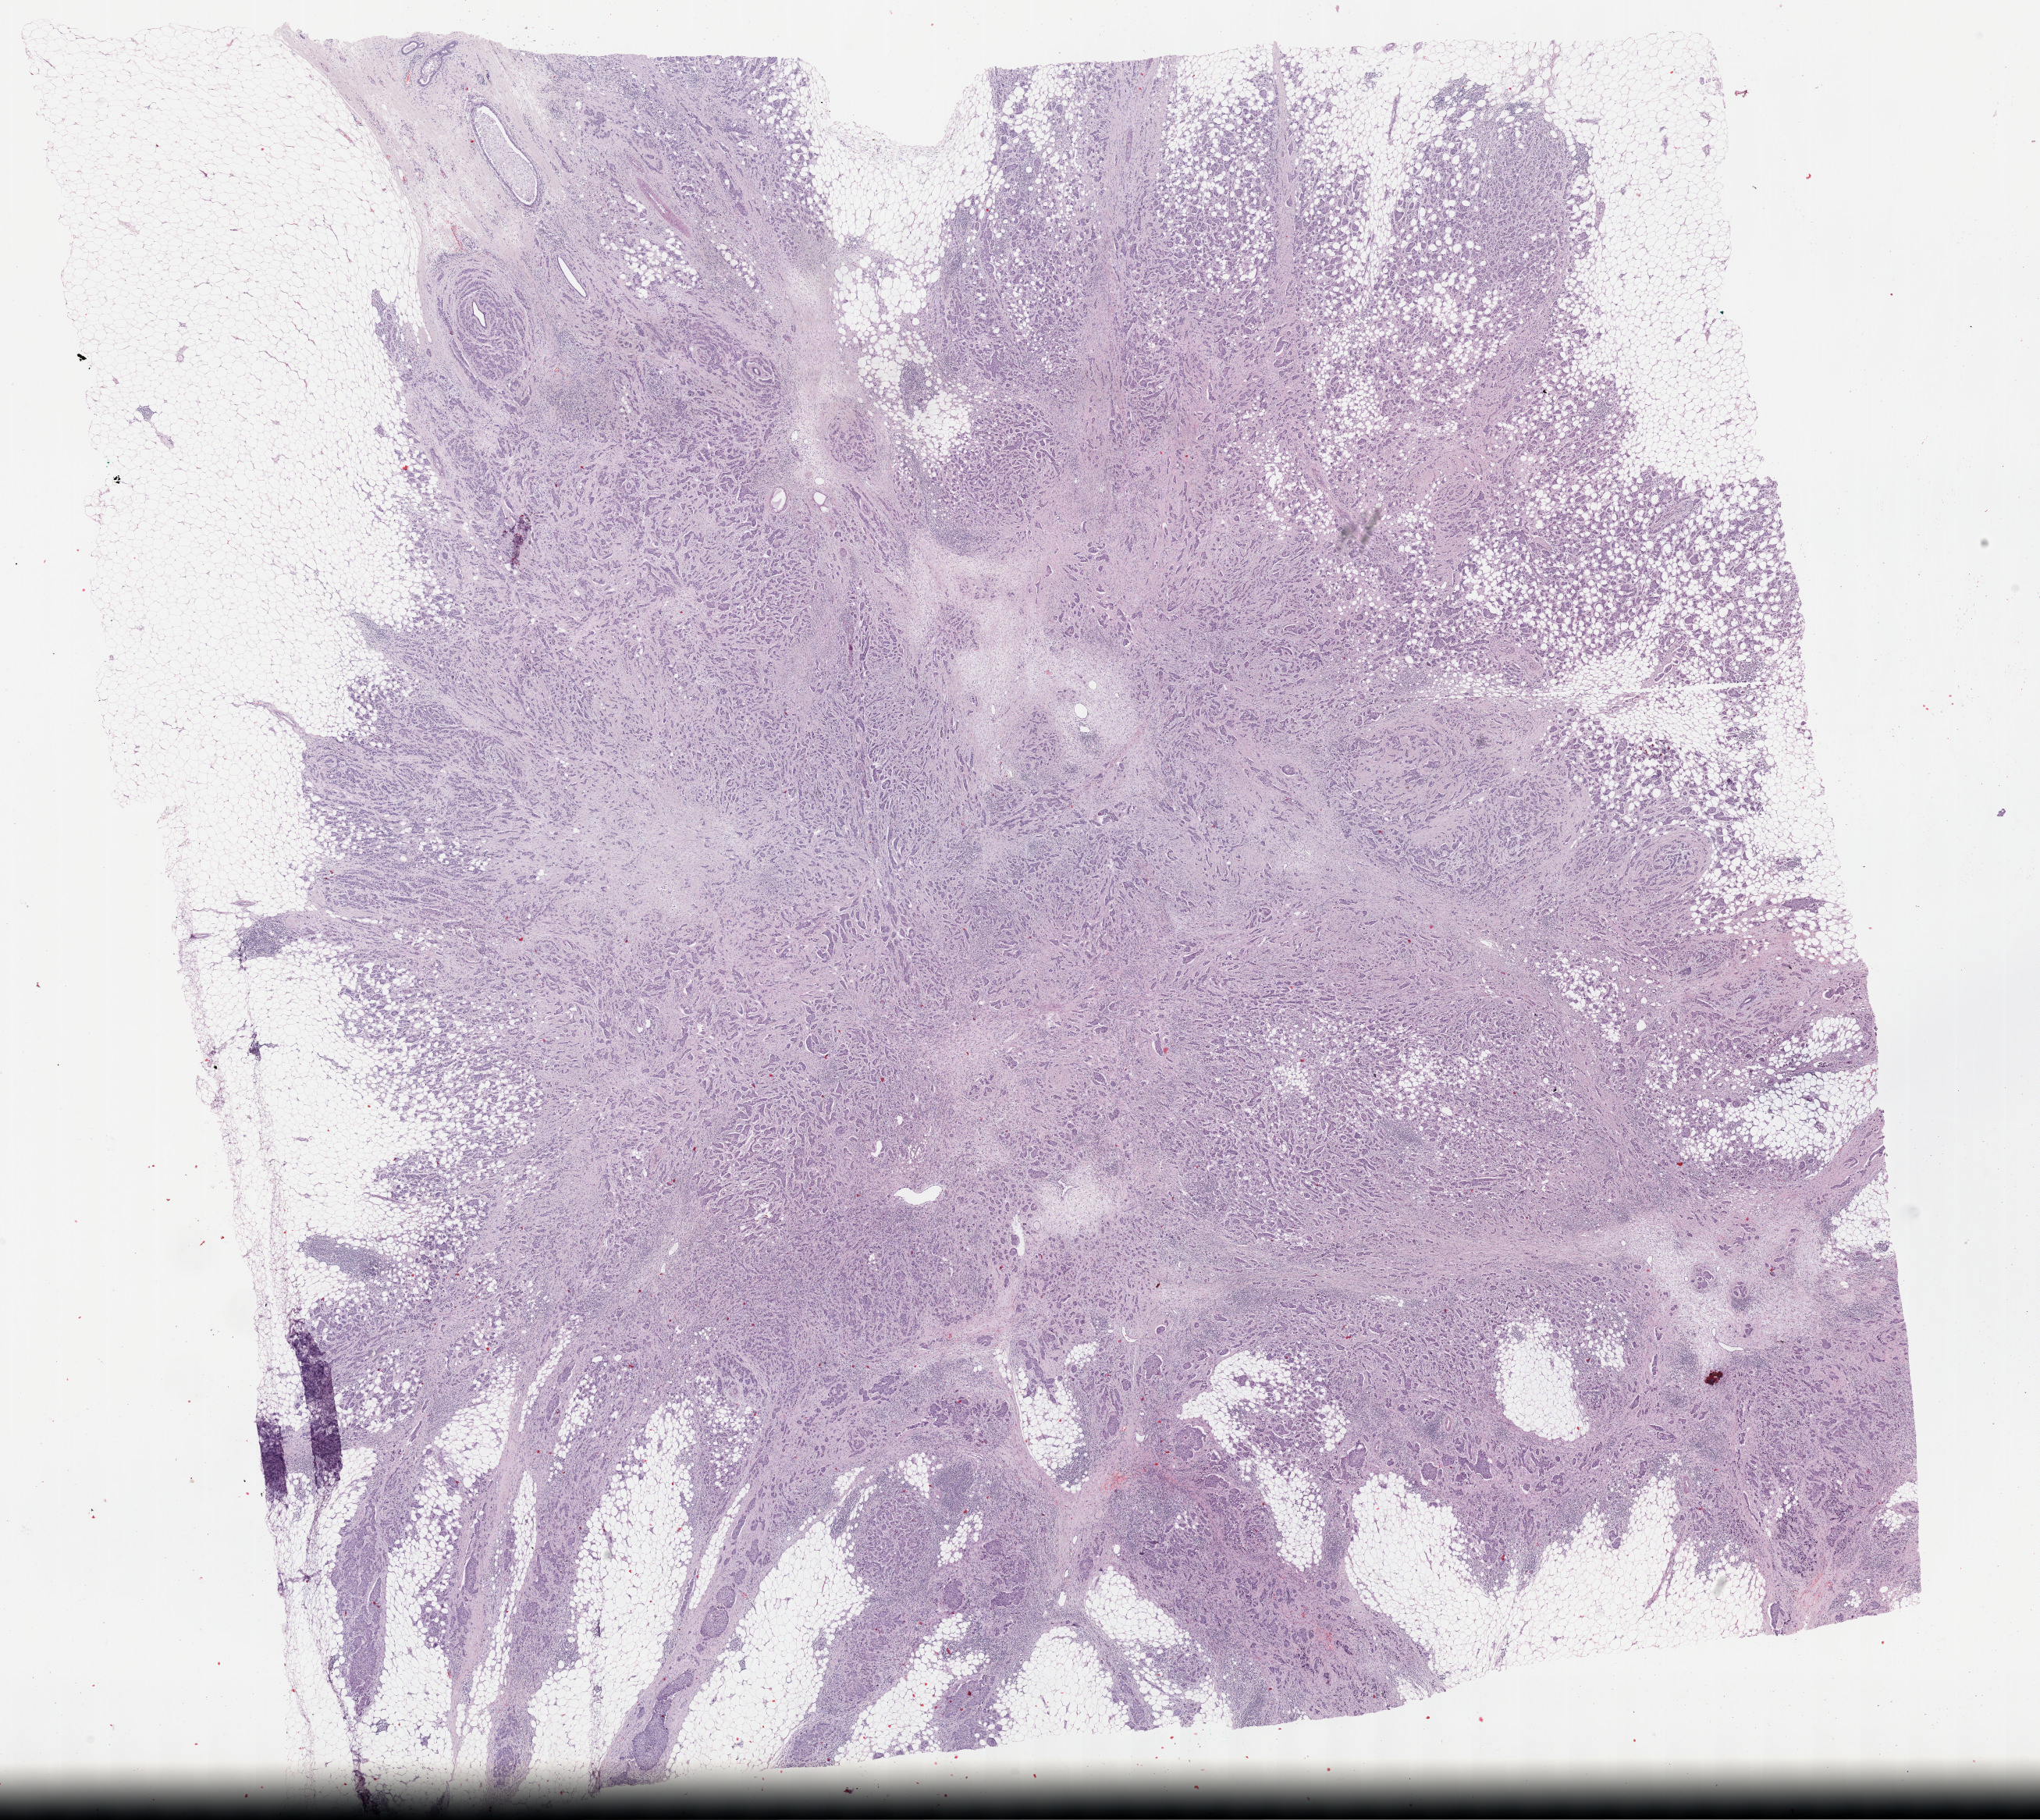
H&E-stained whole-slide image — whole scanned area (about 21.1 x 18.9 mm) shown as a low-resolution overview, formalin-fixed paraffin-embedded (FFPE) diagnostic section, breast, primary tumour sample. Female patient; age at initial diagnosis 54 years.
* AJCC pathologic stage: IIA (7th edition)
* histologic diagnosis: Infiltrating duct carcinoma, NOS
* TNM: T2 N0 M0
* lymph nodes positive (case pathology): 0 of 1 examined